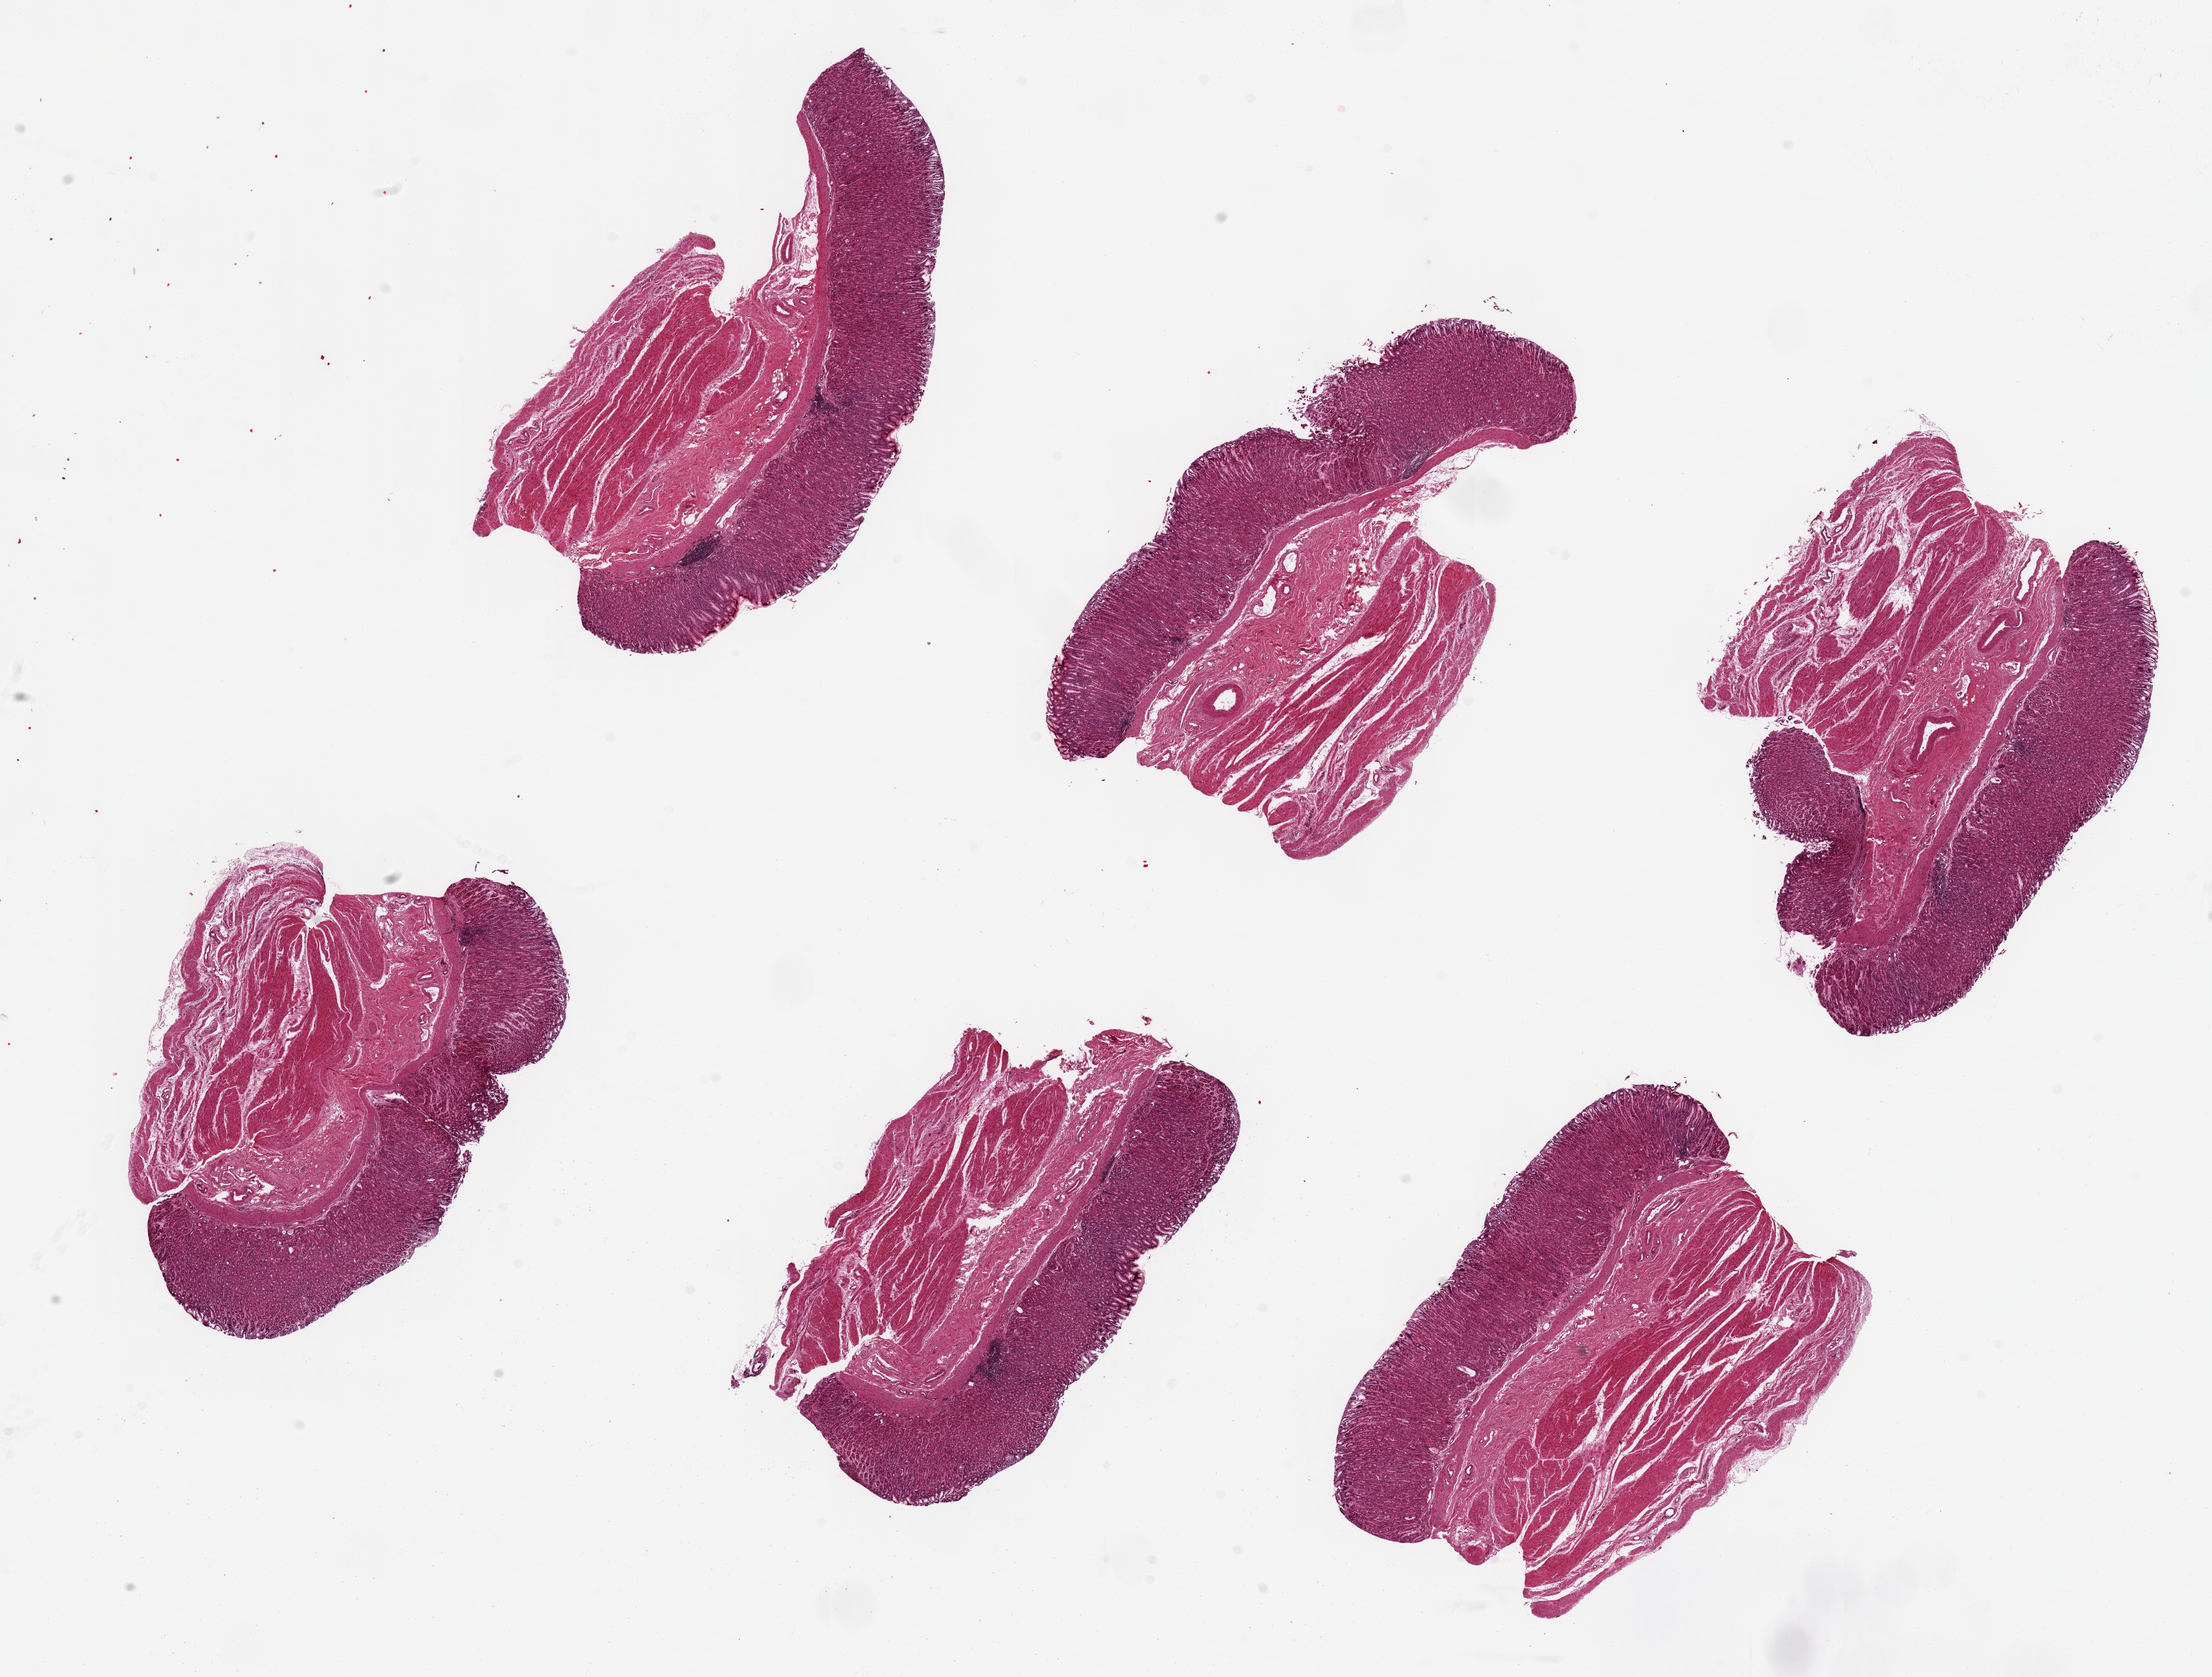
H&E whole-slide image, shown as a low-resolution overview of the whole scanned area (about 23.6 x 17.9 mm); PAXgene-fixed paraffin-embedded (PFPE) section; section of stomach (target tissue); donor tissue sample. Donor: female.
Review note (as recorded): 6 pieces, ~6x4mm pieces. Mucosa extremely well-preserved, ~20-30% of thickness.